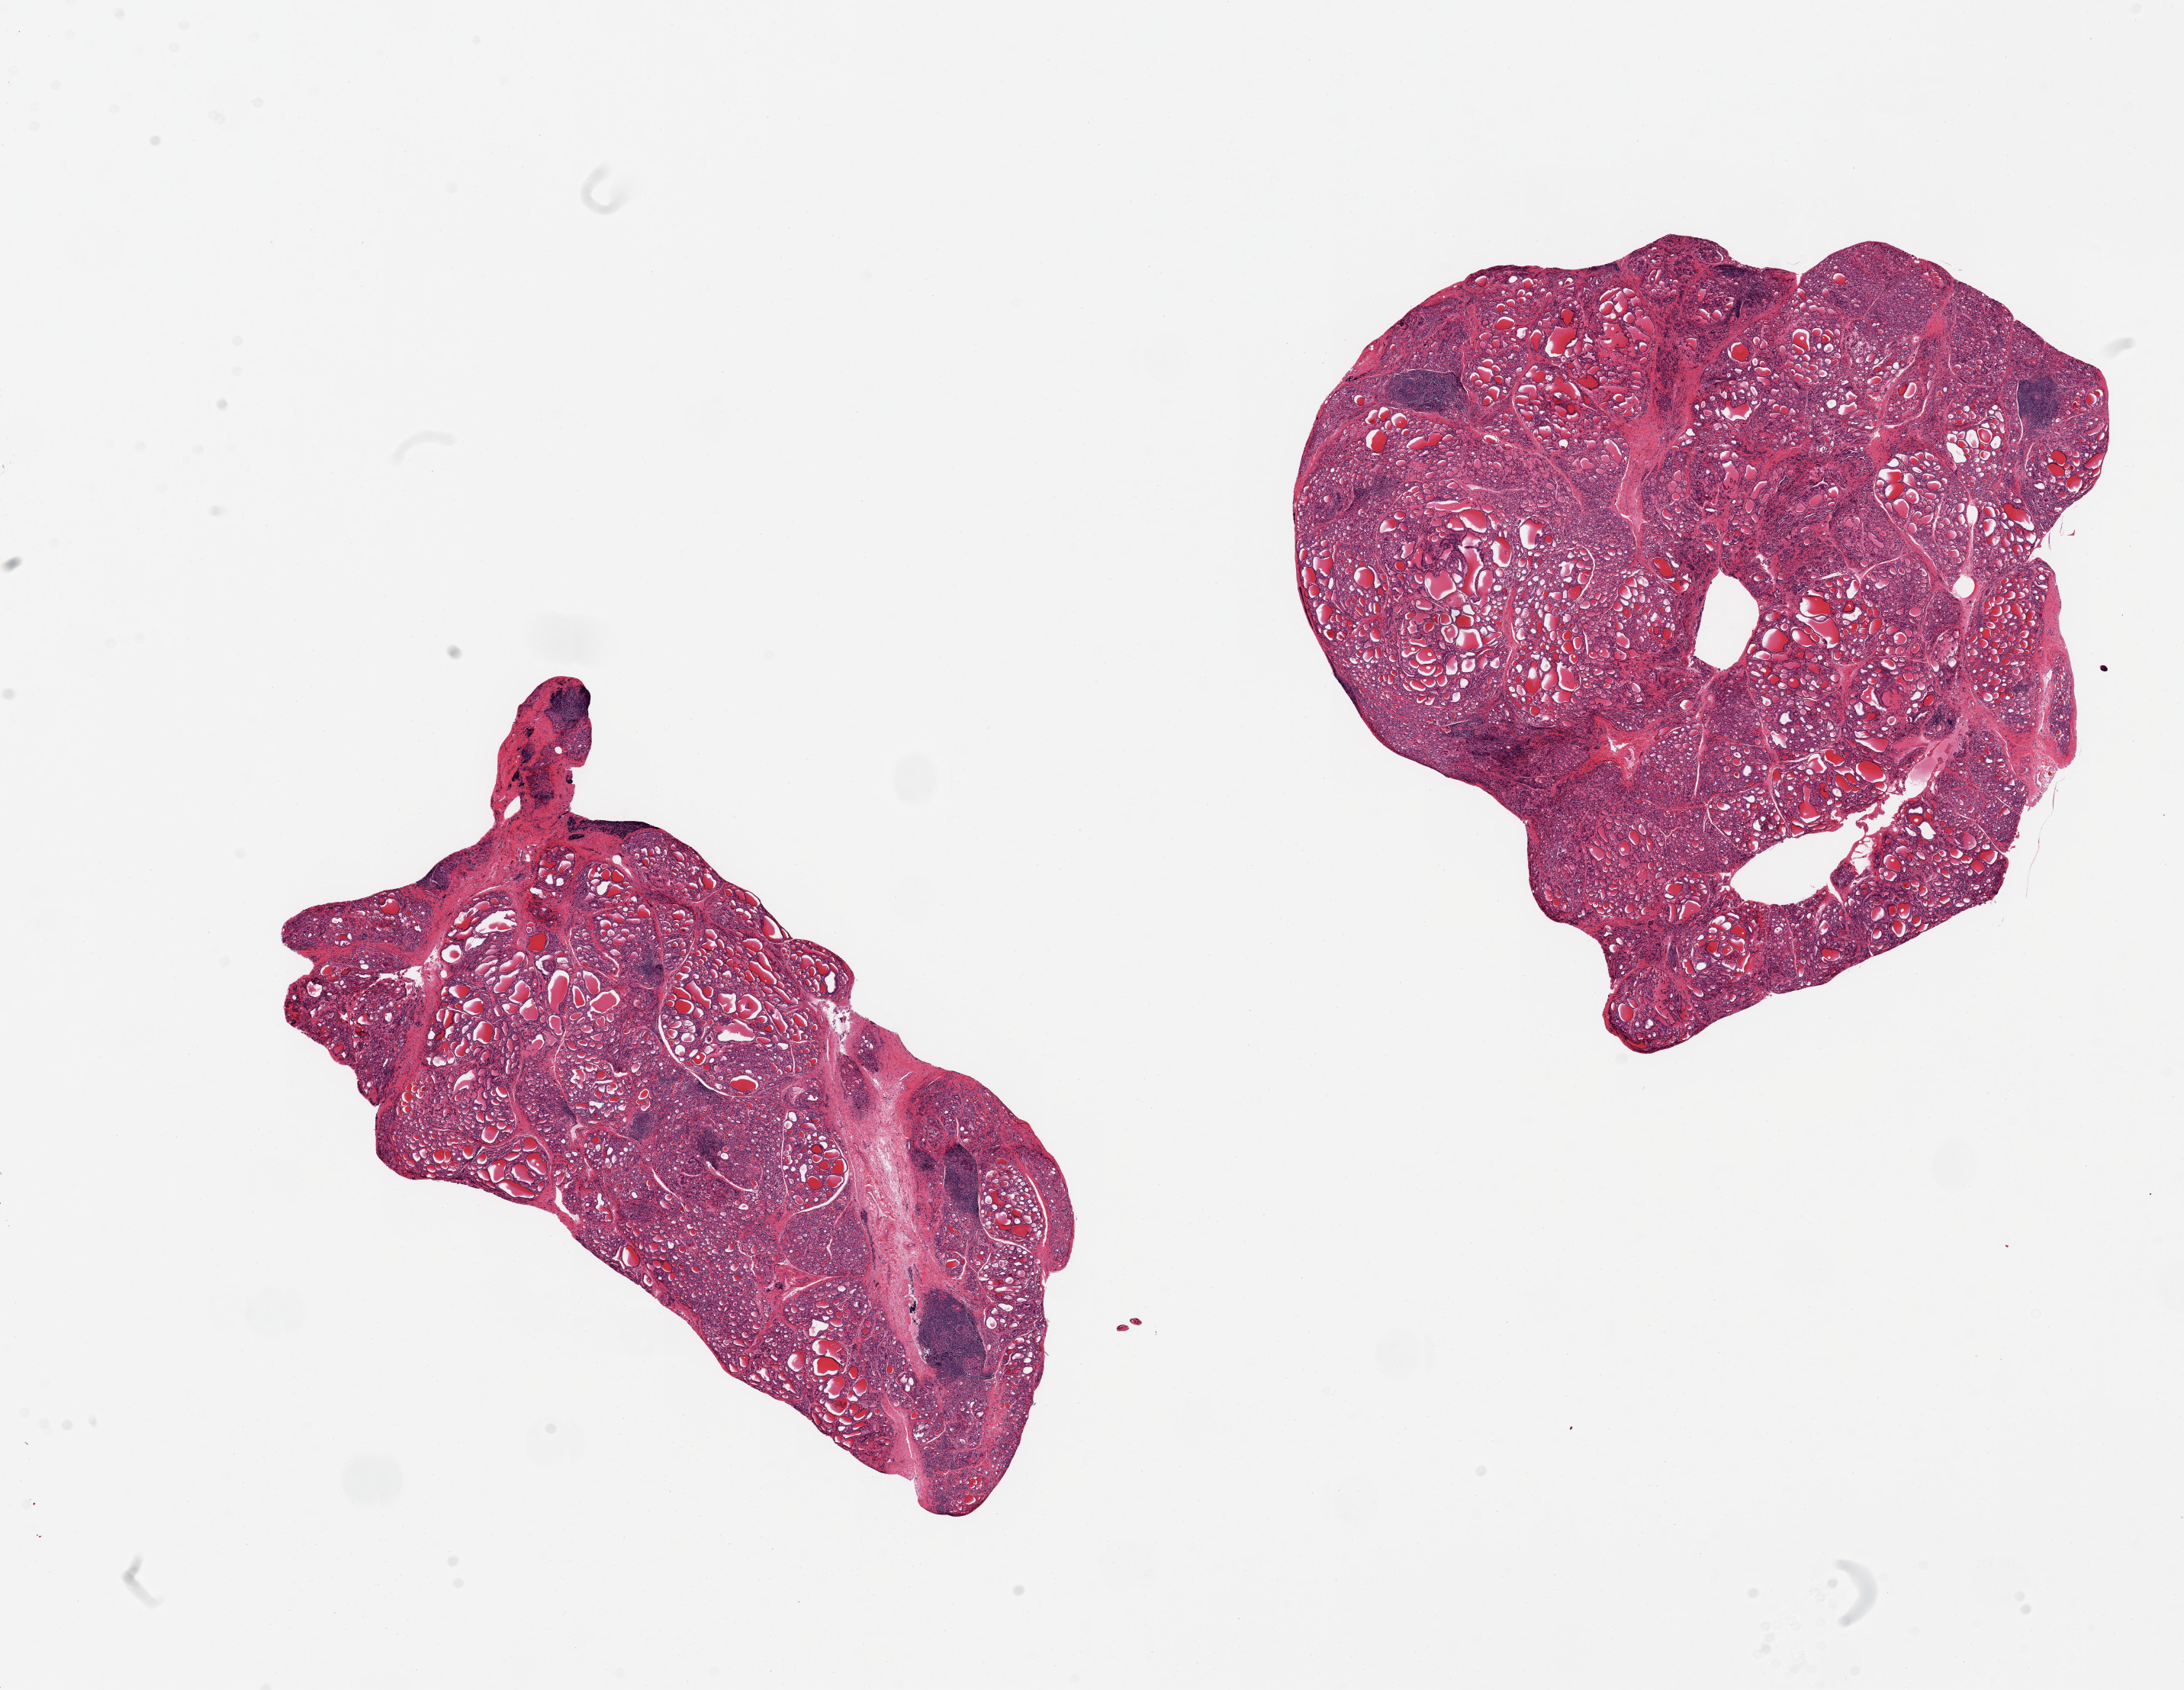
Digitized haematoxylin and eosin-stained section — whole scanned area (about 22.6 x 17.5 mm) shown as a low-resolution overview, PAXgene-fixed paraffin-embedded (PFPE) section, sampled site (target tissue): thyroid, tissue donor sample. Donor: female.
Pathologist's review note for this sample: 2 pieces; moderate degree of Hashimoto (lymphocytic) thyroiditis.